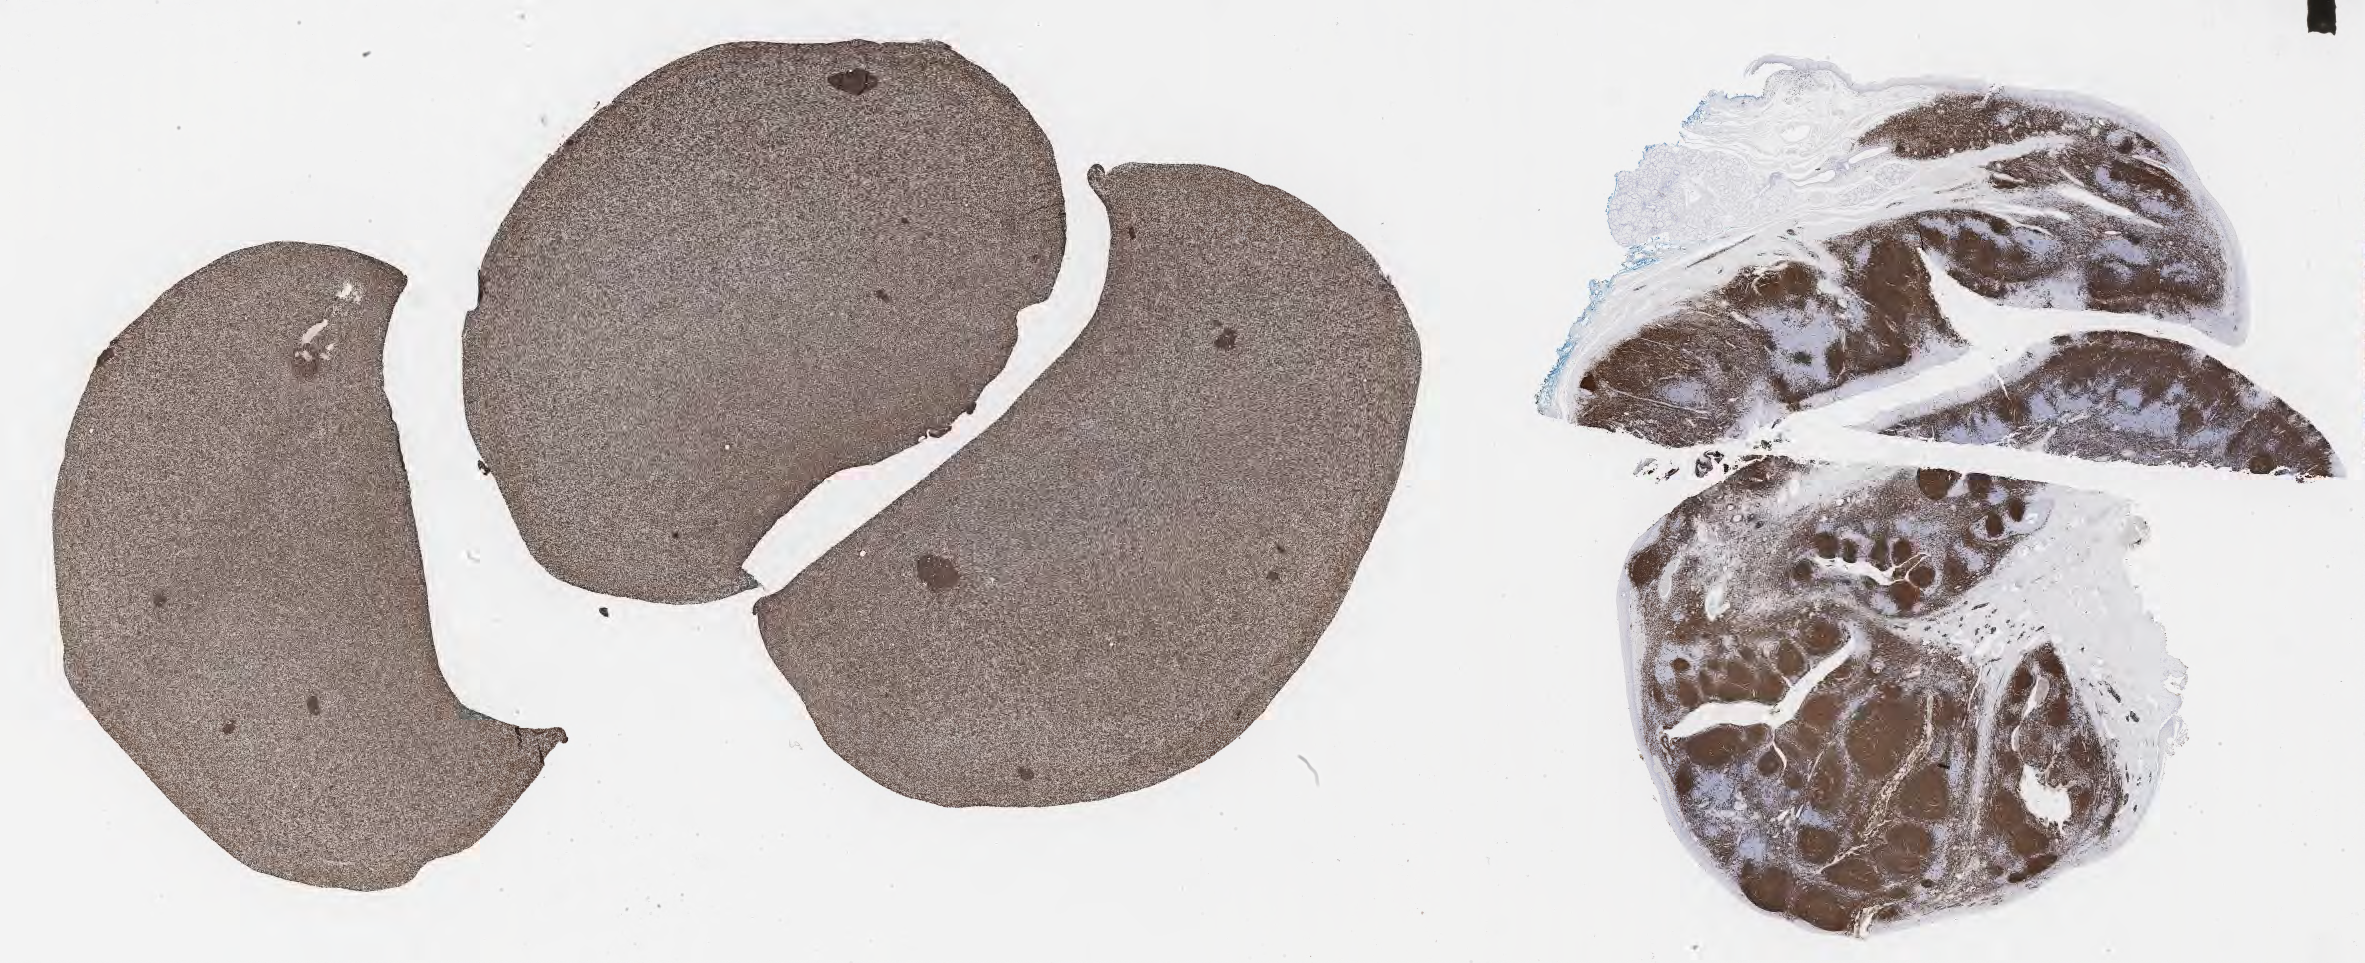
Whole-slide image, immunohistochemical stain for CD20 — whole scanned area (about 38.2 x 15.6 mm) shown as a low-resolution overview. Tumor tissue. Patient: male, aged 17.
- diagnosis: Burkitt lymphoma, NOS